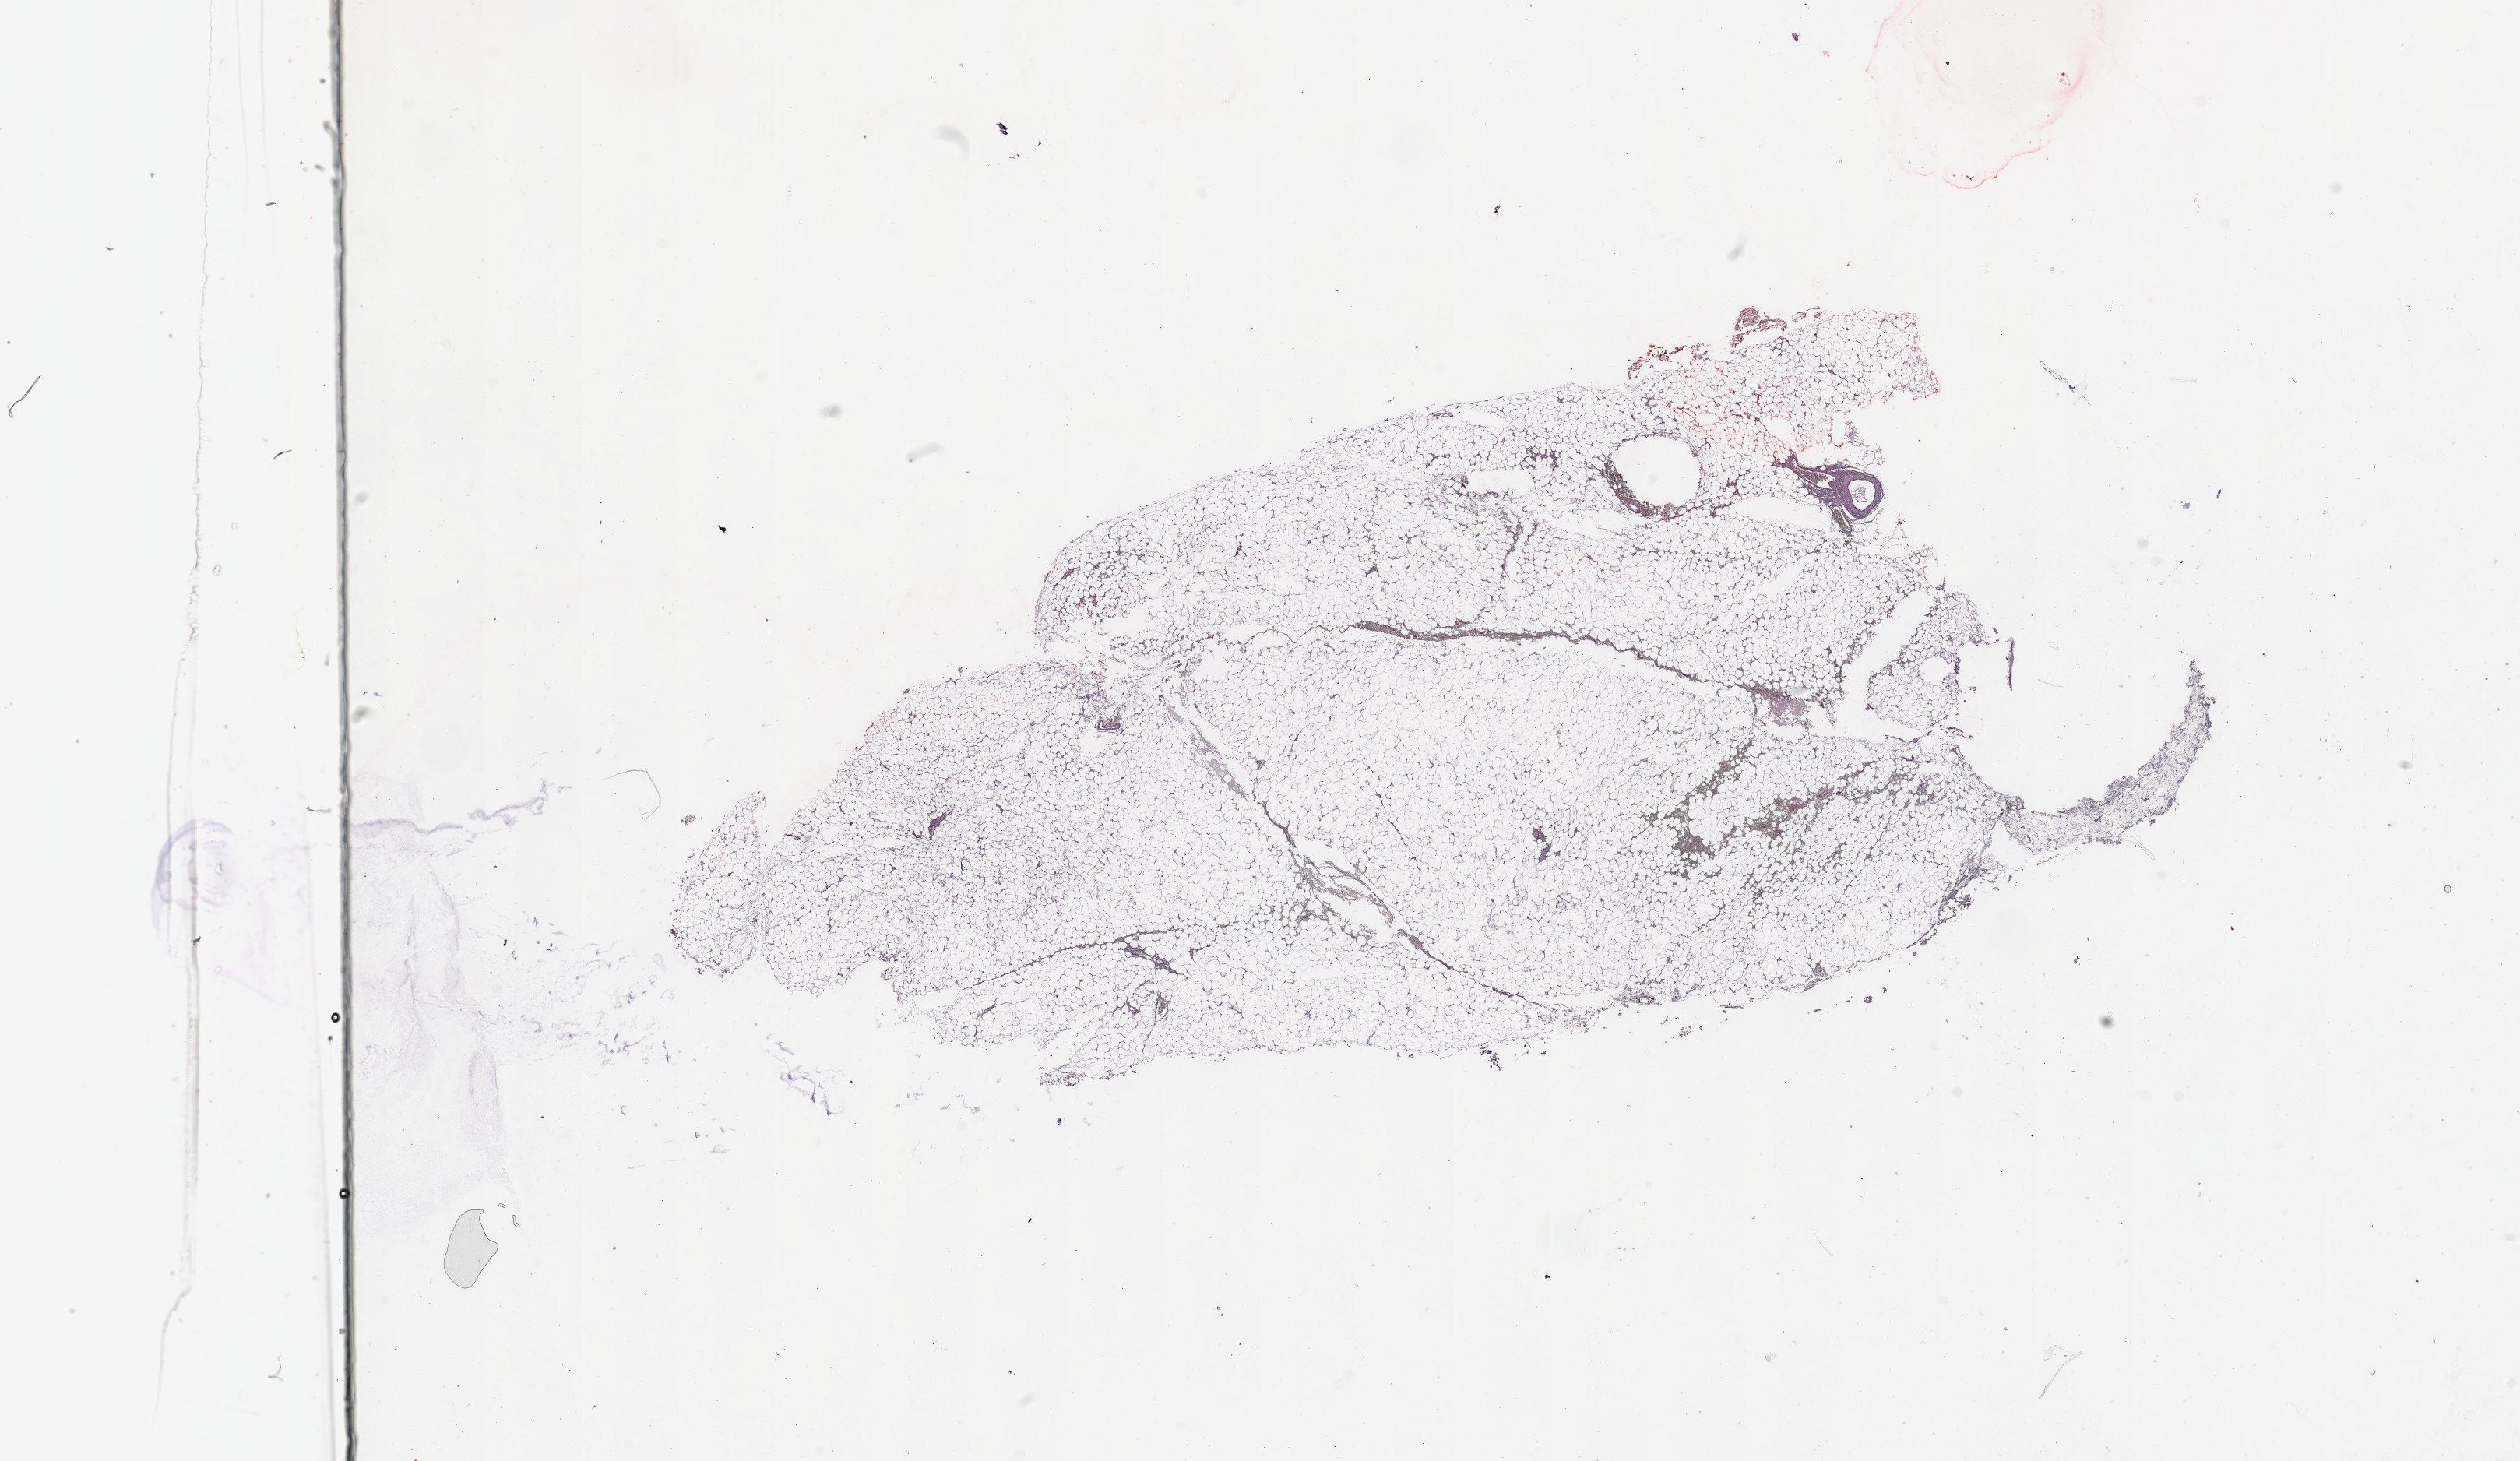
Digitized Hematoxylin and eosin (H&E) stained tissue section (whole slide) — shown as a low-resolution overview of the whole scanned area (about 25.6 x 14.8 mm, acquisition: 20x scan). Kidney, normal (non-tumour) tissue. Patient: male, age 49 years.
This section: normal (non-tumour) tissue from the same patient. Patient diagnosis: Renal cell carcinoma, NOS.